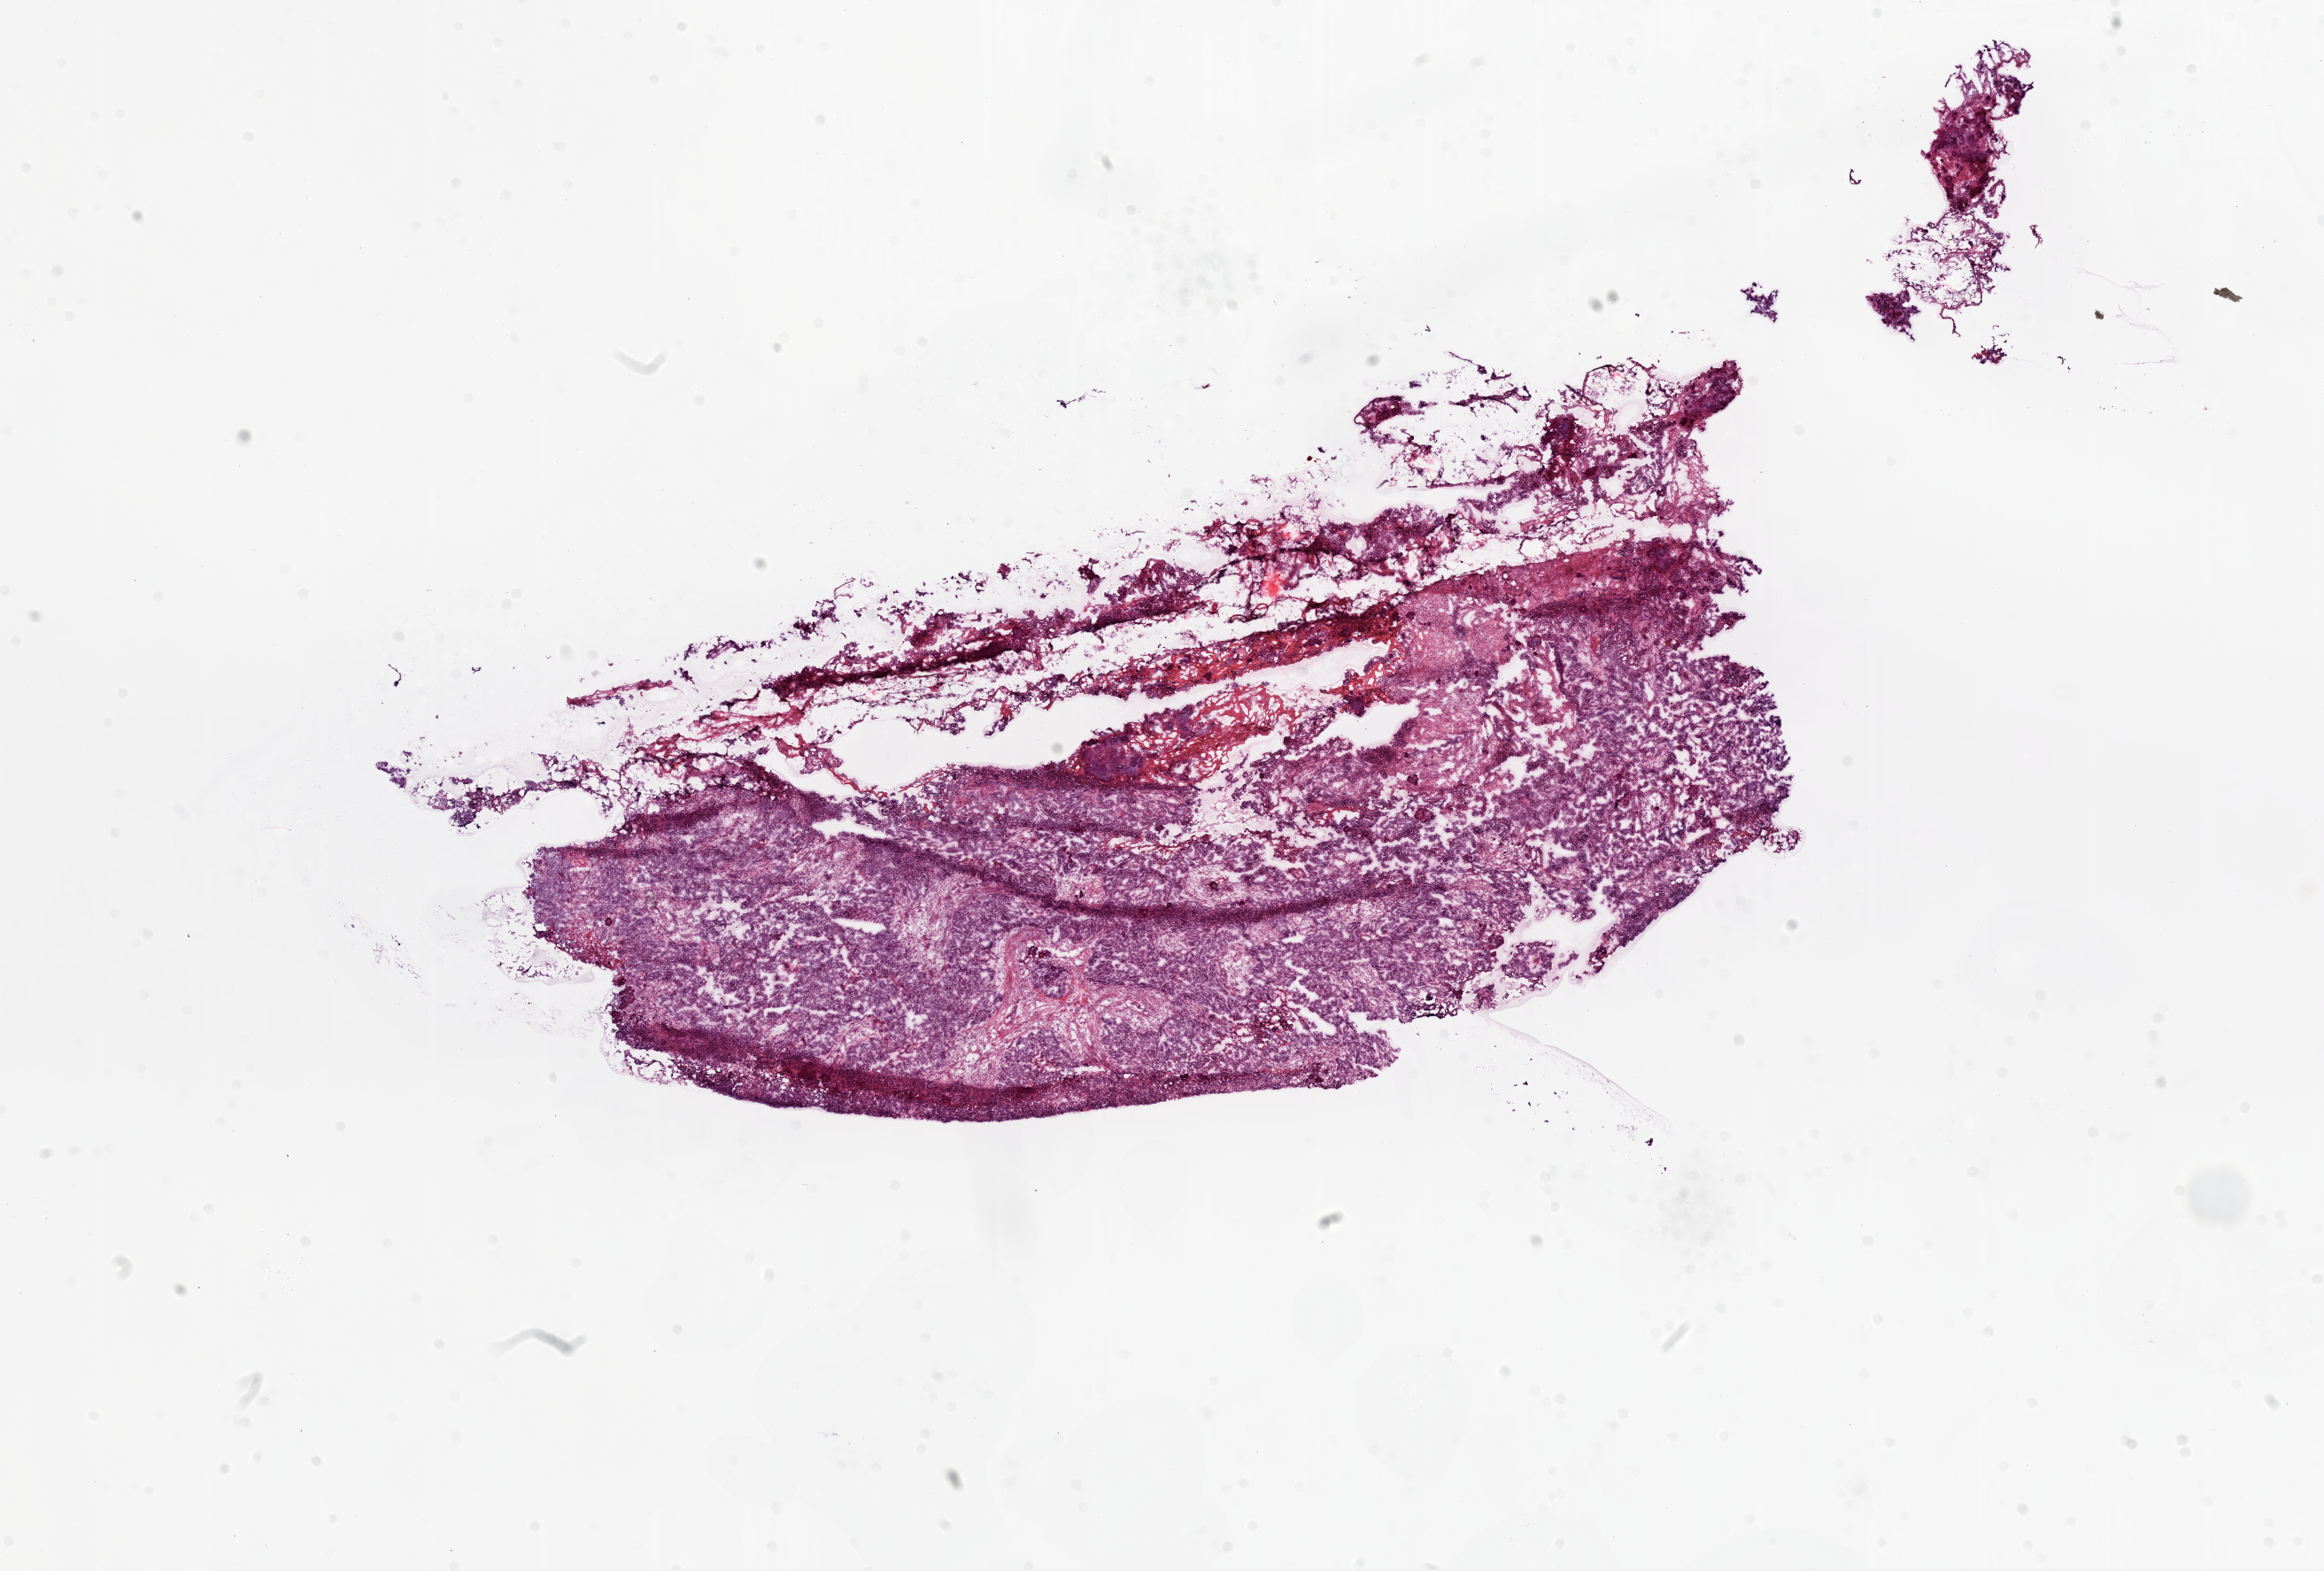
H&E whole-slide image, whole scanned area (about 21.1 x 14.2 mm) shown as a low-resolution overview; frozen section from the bottom of the tissue portion; ovary, primary tumour sample. Patient: female, age at initial diagnosis 74 years. Histologic grade: G3 (poorly differentiated). Slide review estimates, as recorded: tumour cells 88%, tumour nuclei 80%, normal cells 0%, stromal cells 10%, necrosis 2%.
FIGO stage: IIIC. Histologic diagnosis: Serous cystadenocarcinoma, NOS.